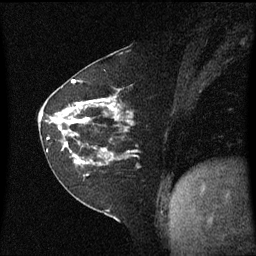
Breast MRI (dynamic contrast-enhanced), one sagittal slice. Slice 26 of 60 in the series (ordered by position). Dynamic contrast-enhanced series, image 2 of 3 at this slice position (ordered by acquisition). 1.5 T. TE 4.2 ms, TR 8.4 ms. 2 mm slice thickness. 256 × 256 image matrix, field of view 210 × 210 mm. Female patient, age 60 years. From the clinical record (not read from this slice): setting: breast cancer imaged before/during neoadjuvant chemotherapy; receptor status: triple-negative.
Structures marked on this image (semi-automatically segmented with operator editing):
- analysis volume of interest (the breast-tissue region the enhancement analysis was run in; not a lesion): box from (x=45, y=99) to (x=142, y=182) px
- tumour enhancement mask (voxels above the 70 % enhancement threshold inside the analysis volume of interest): (x=52, y=100)–(x=118, y=160)